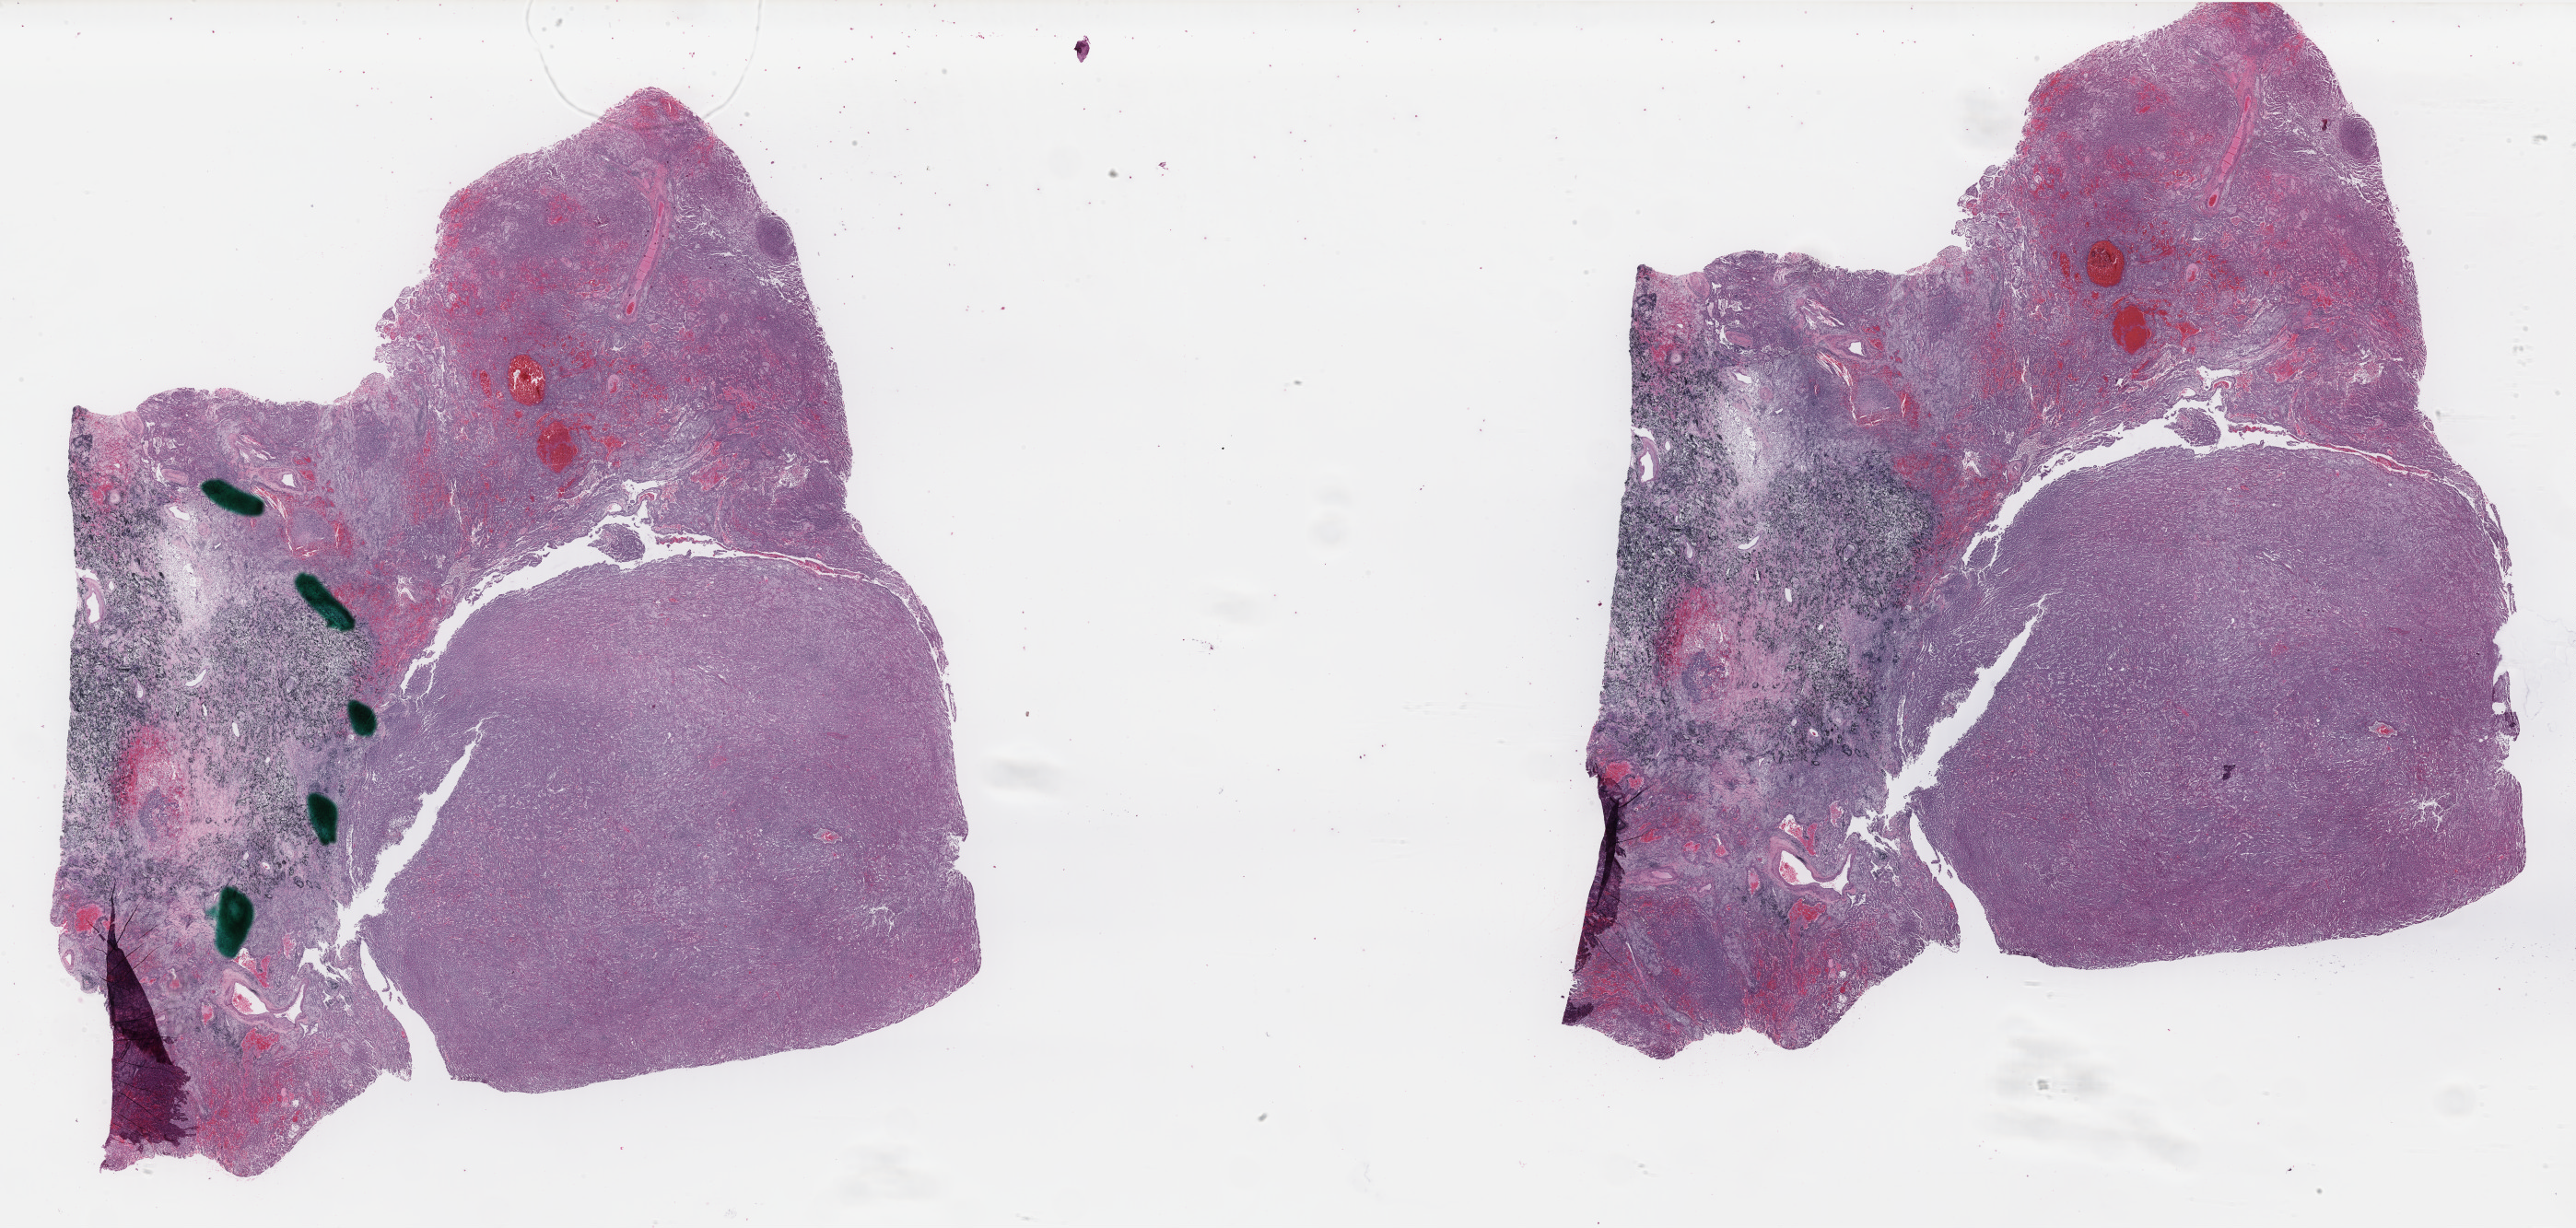
Digitized H&E-stained tissue section (whole slide) — a low-resolution overview of the entire scanned area, about 44.2 x 21.1 mm (slide scanned at 40x), formalin-fixed paraffin-embedded (FFPE) diagnostic section, sample: primary tumour, kidney. Male patient; age at initial diagnosis 50 years.
* AJCC pathologic stage: II
* histologic diagnosis: Papillary adenocarcinoma, NOS
* TNM: T2b NX M0